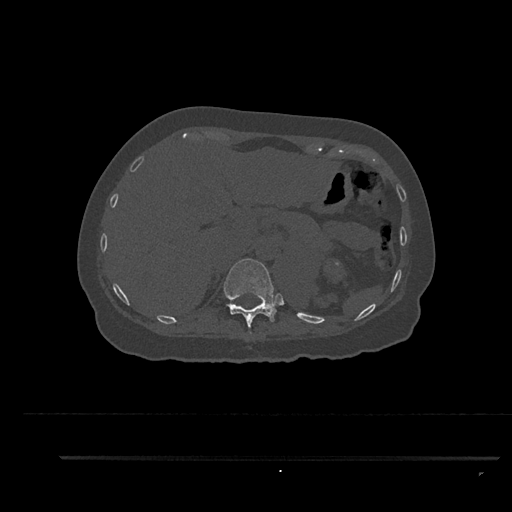
CT including the spine, one axial slice; position 314 of 797 along the scan axis; reconstruction kernel Br40s/3; 120 kVp; bone window (W 1800 / L 400 HU); 0.5 mm slice thickness; 512 × 512 image matrix. Female patient, age 44 years. Case-level facts recorded for this patient, not image findings: primary cancer: renal; vertebrae with lytic lesions (as recorded): L1.
Outlined on this slice (semi-automatic segmentation, software-assisted and operator-edited):
- T11 vertebra: bounding box <224,259,277,334> (left, top, right, bottom; pixels)